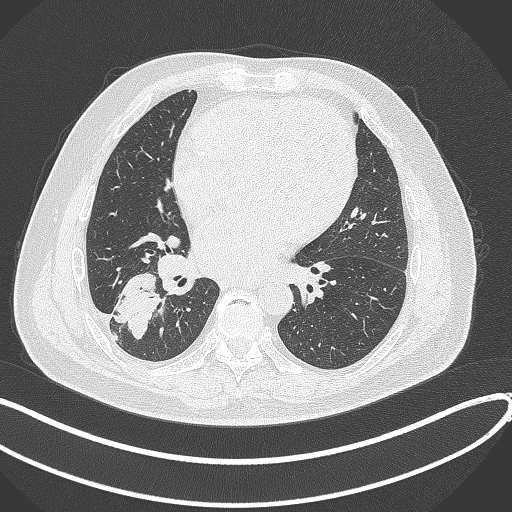
Chest CT, one axial slice. Position 159 of 360 along the scan axis. Reconstruction kernel B70f. Lung window (W 1500 / L -600 HU). 1 mm slice thickness. 512 × 512 image matrix, field of view 400 × 400 mm. Patient: male, 59 years.
Outlined on this slice (bounding box drawn by a radiologist):
- lung tumour (recorded histology: adenocarcinoma): bounding box (x1, y1, x2, y2) in pixels: (109, 268, 164, 341)